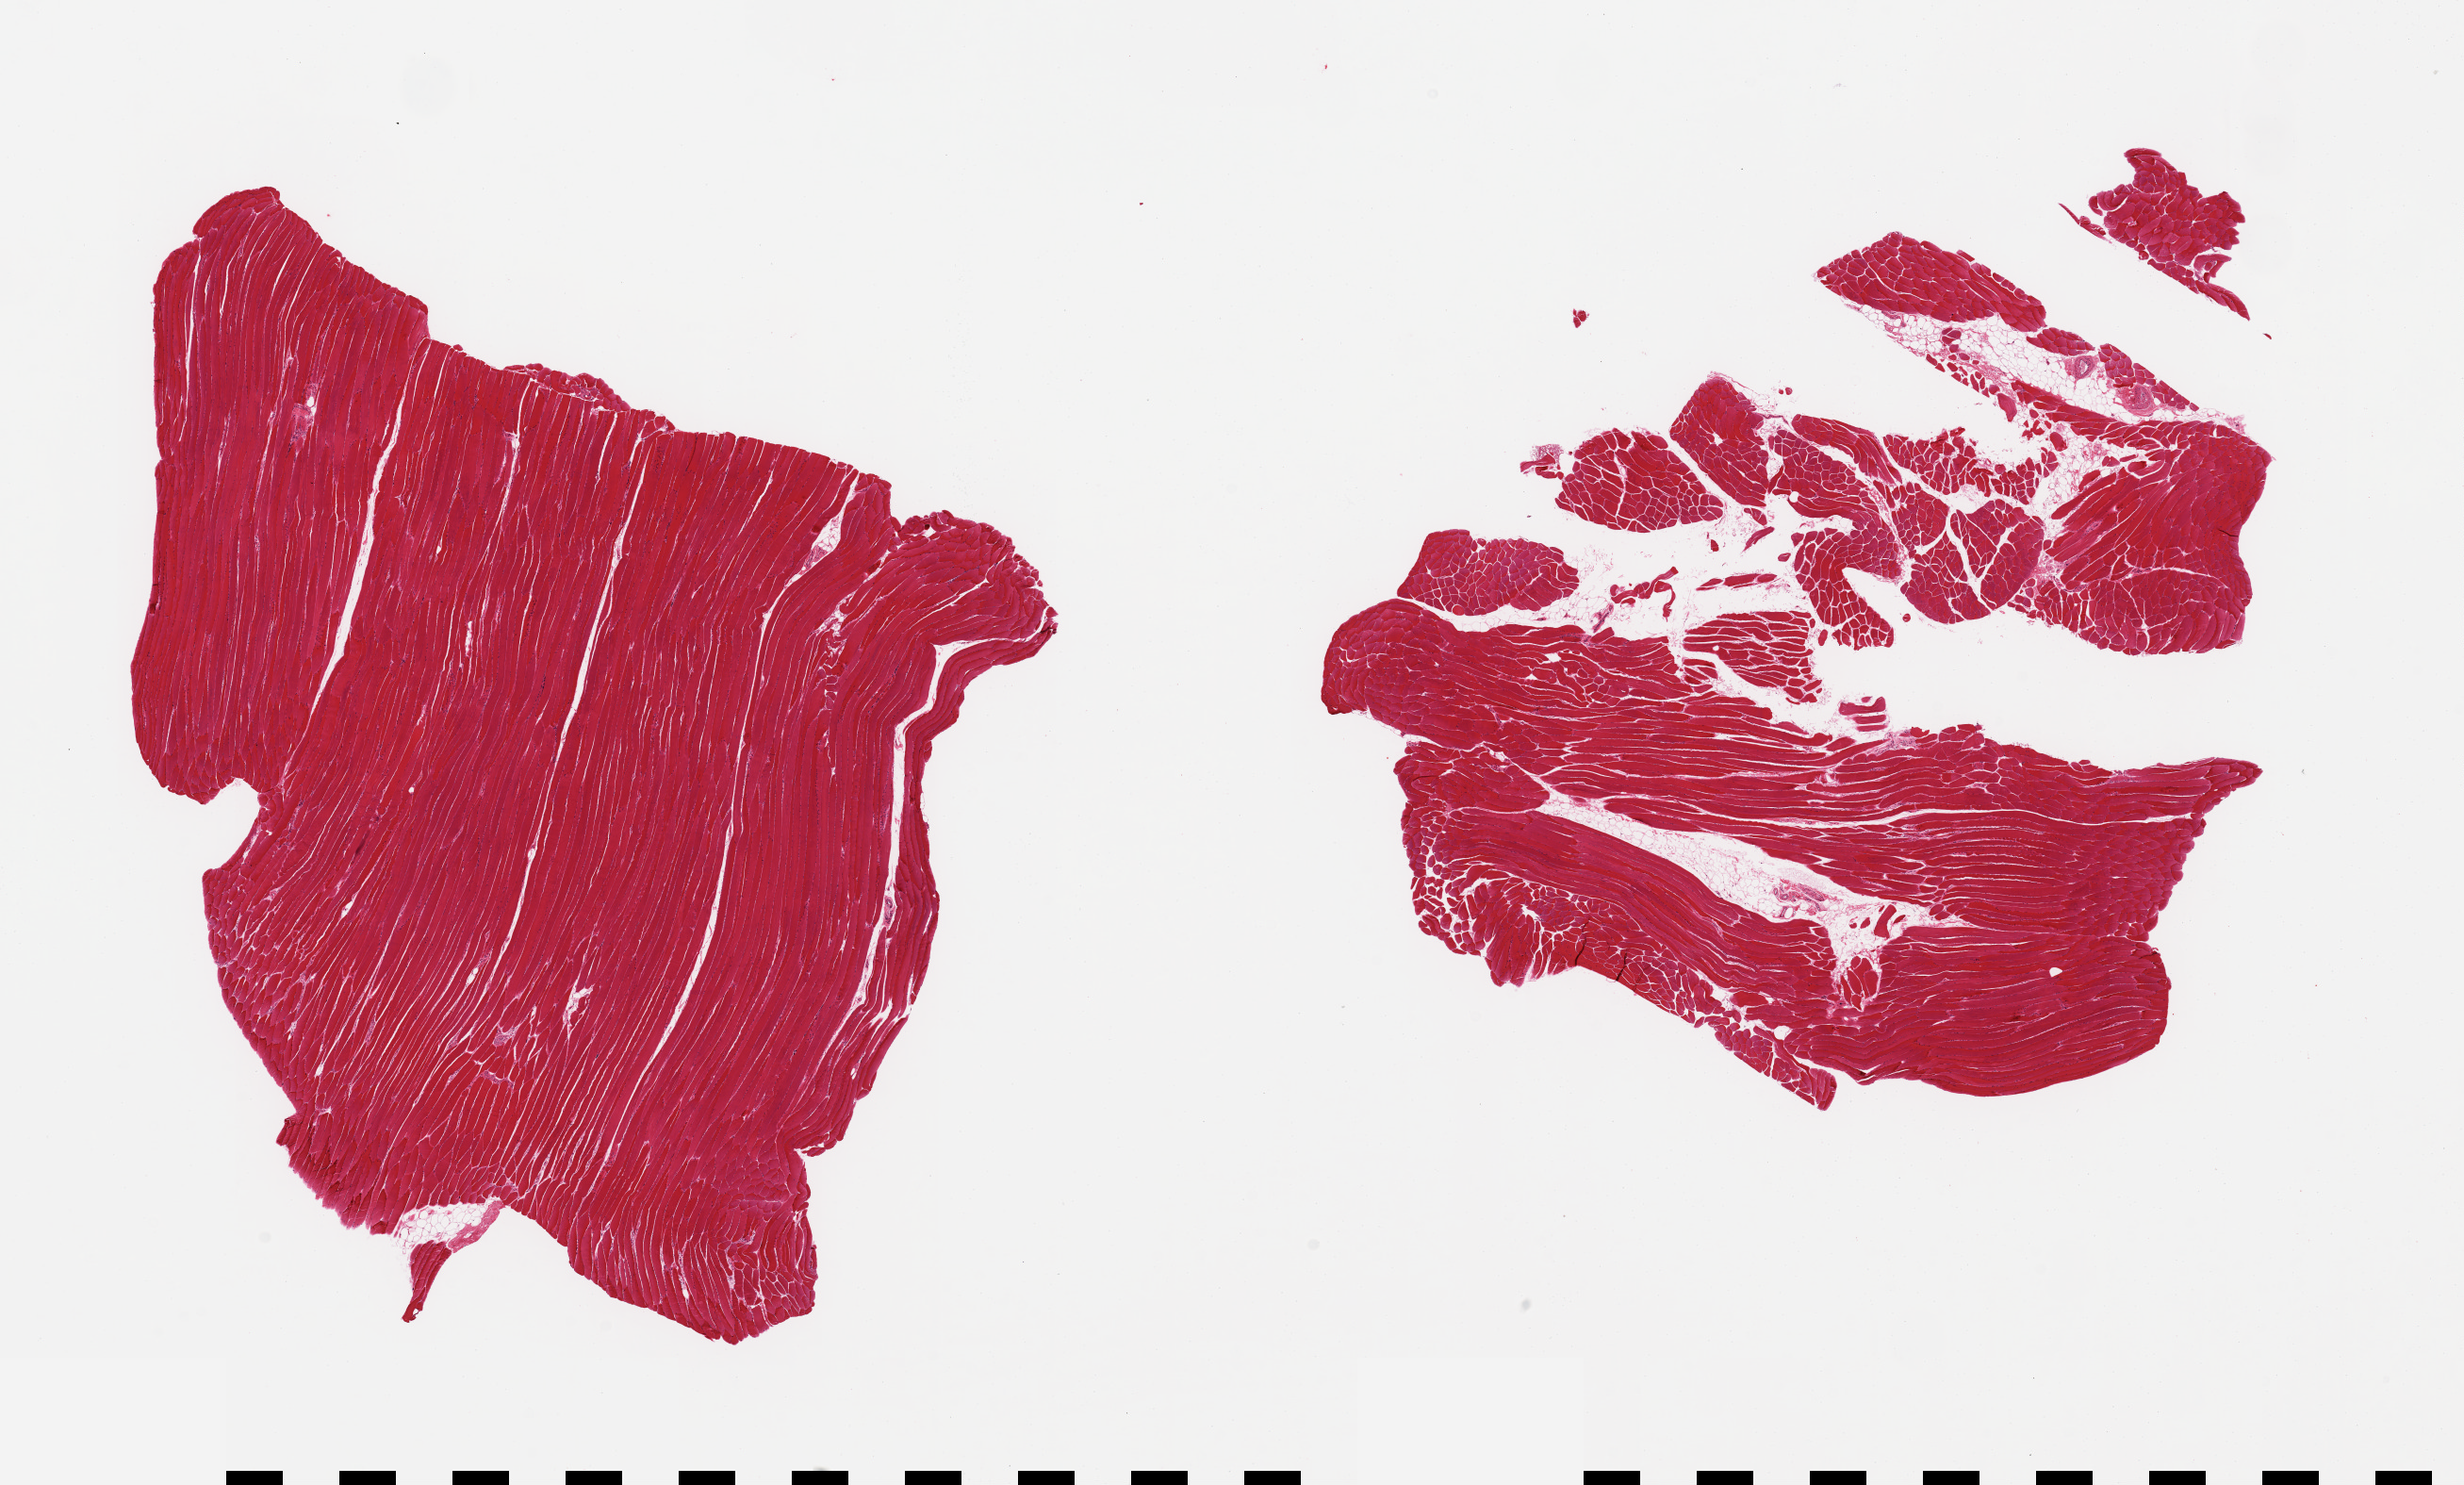
Whole-slide image, hematoxylin and eosin (H&E) stain — whole scanned area (about 20.7 x 12.5 mm) shown as a low-resolution overview; PAXgene-fixed, paraffin-embedded tissue; section of skeletal muscle (target tissue); tissue donor sample.
* reviewer comment on this tissue sample: 2 pieces, interstitial fat/vascular elements, ~10-15% of tissue